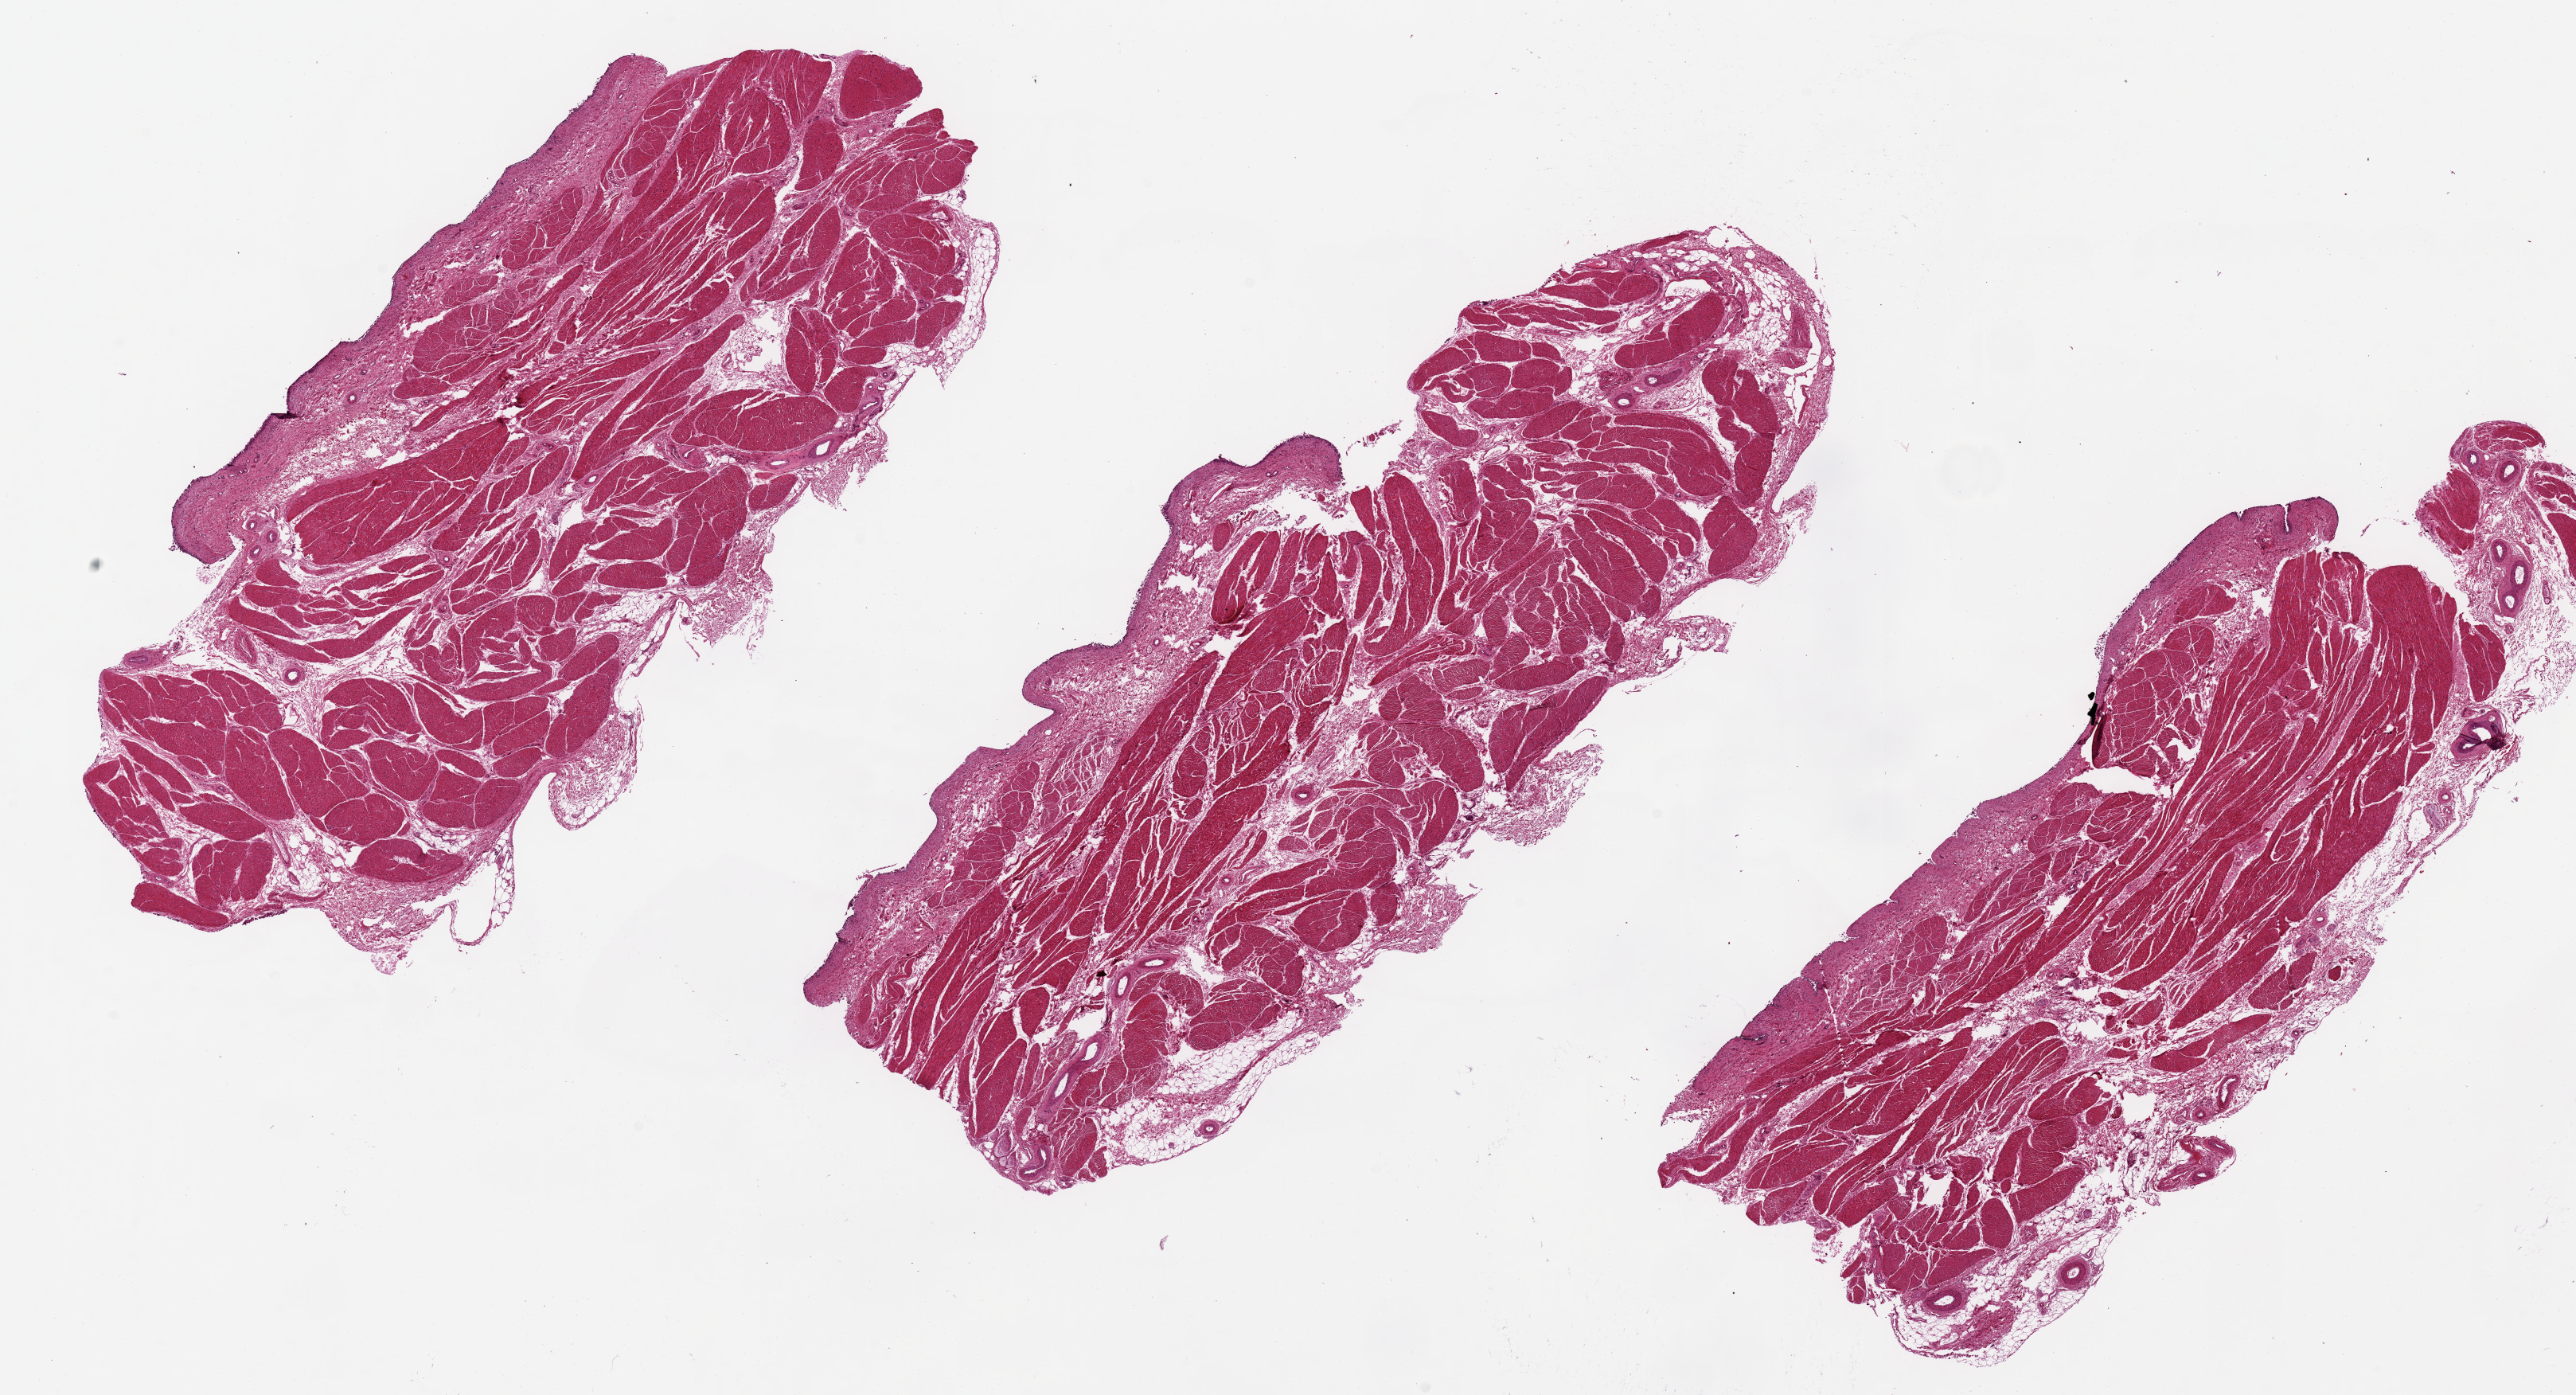
Digitized H&E-stained section, low-resolution overview of the scanned area, about 25.6 x 13.9 mm (from a 20x scan). PAXgene-fixed, paraffin-embedded tissue. Target tissue: urinary bladder. Tissue donor sample.
Reviewer comment on this tissue sample: Mucosa 90% sloughed/autolyzed.